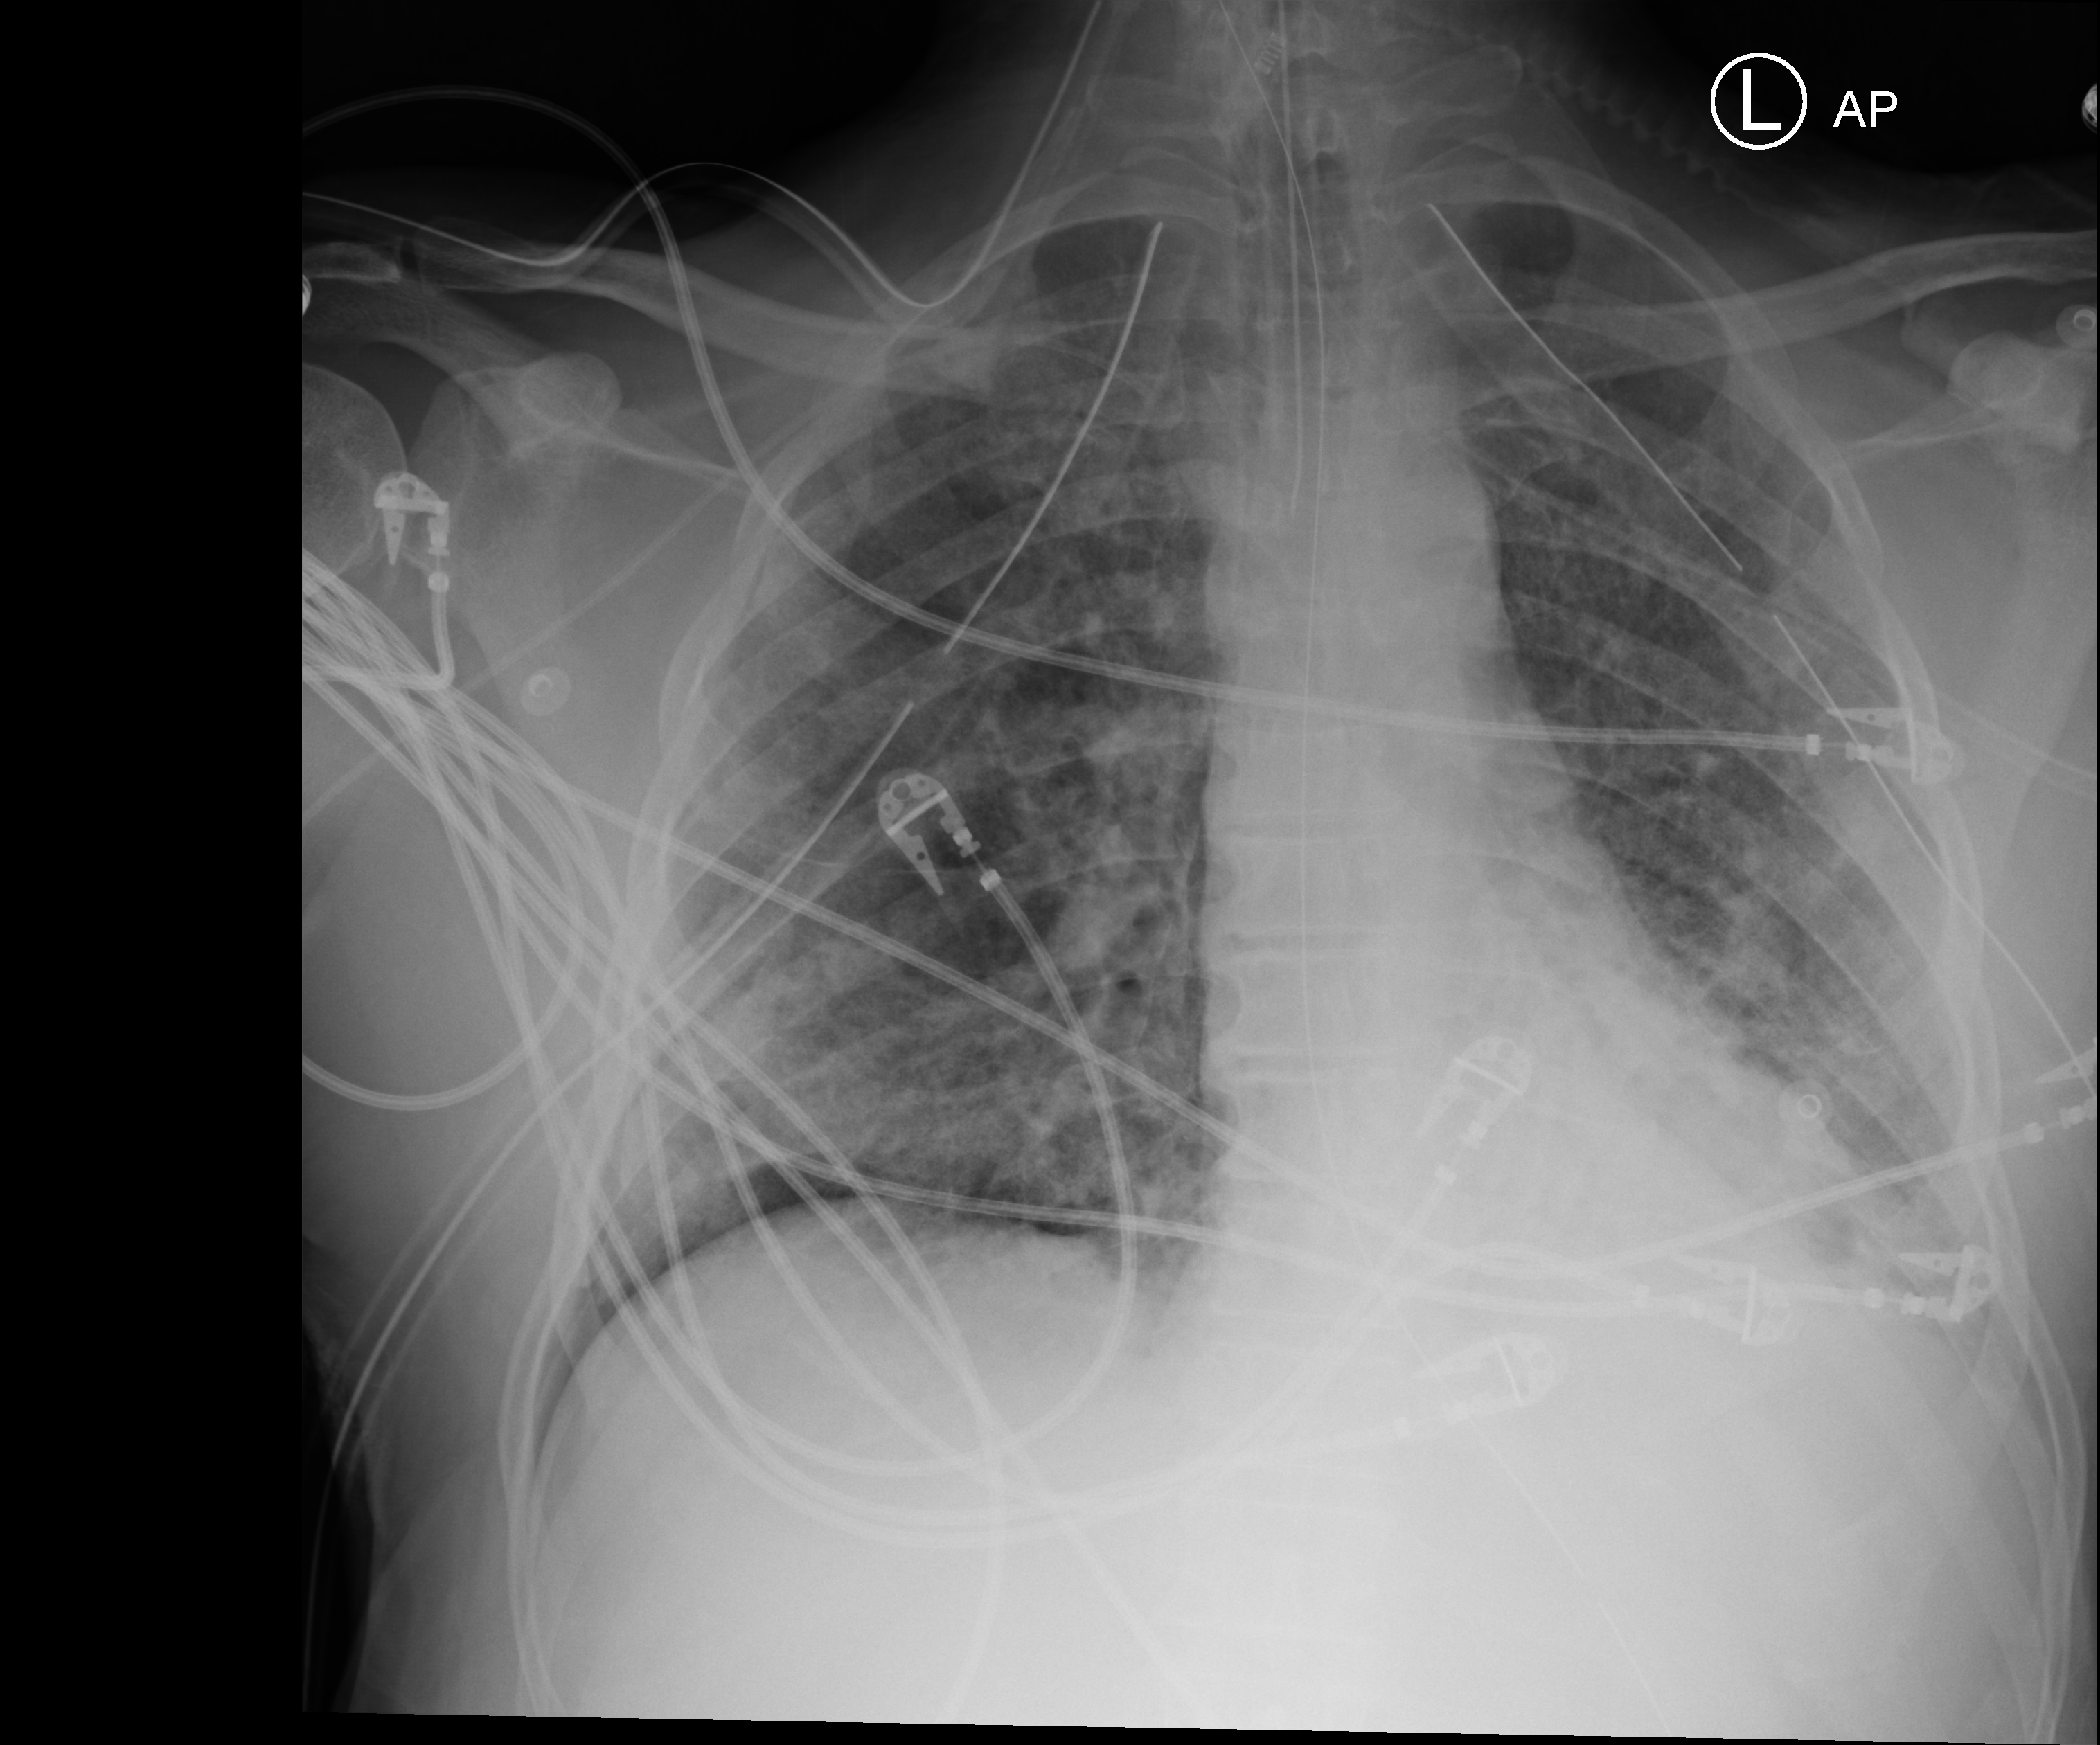
Chest X-ray (portable); anteroposterior (AP) projection. Male patient hospitalised with COVID-19, age 18–59 years.
Hospital-stay facts (about this admission, not read from this image; timing relative to this image not recorded): admitted to intensive care during this hospital stay: yes.